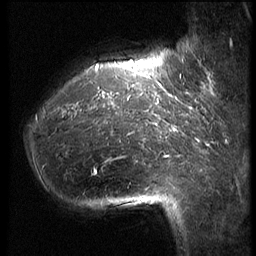
Breast MRI (dynamic contrast-enhanced), one sagittal slice; slice 13 of 62 in the series (ordered by position); 3 images stored at this slice position (order not interpretable as contrast timing); 1.5 T; TE 4.2 ms, TR 9 ms; 2.5 mm slice thickness; 256 × 256 image matrix, field of view 180 × 180 mm. Patient: female, 39 years. From the clinical record (not read from this slice): setting: breast cancer imaged before/during neoadjuvant chemotherapy; receptor status: HER2-positive.
Structures marked on this image (semi-automatic segmentation, software-assisted and operator-edited):
- analysis volume of interest (the breast-tissue region the enhancement analysis was run in; not a lesion): box from (x=26, y=64) to (x=171, y=228) px
- tumour enhancement mask (voxels above the 140 % enhancement threshold inside the analysis volume of interest): (x=65, y=64)–(x=171, y=174)